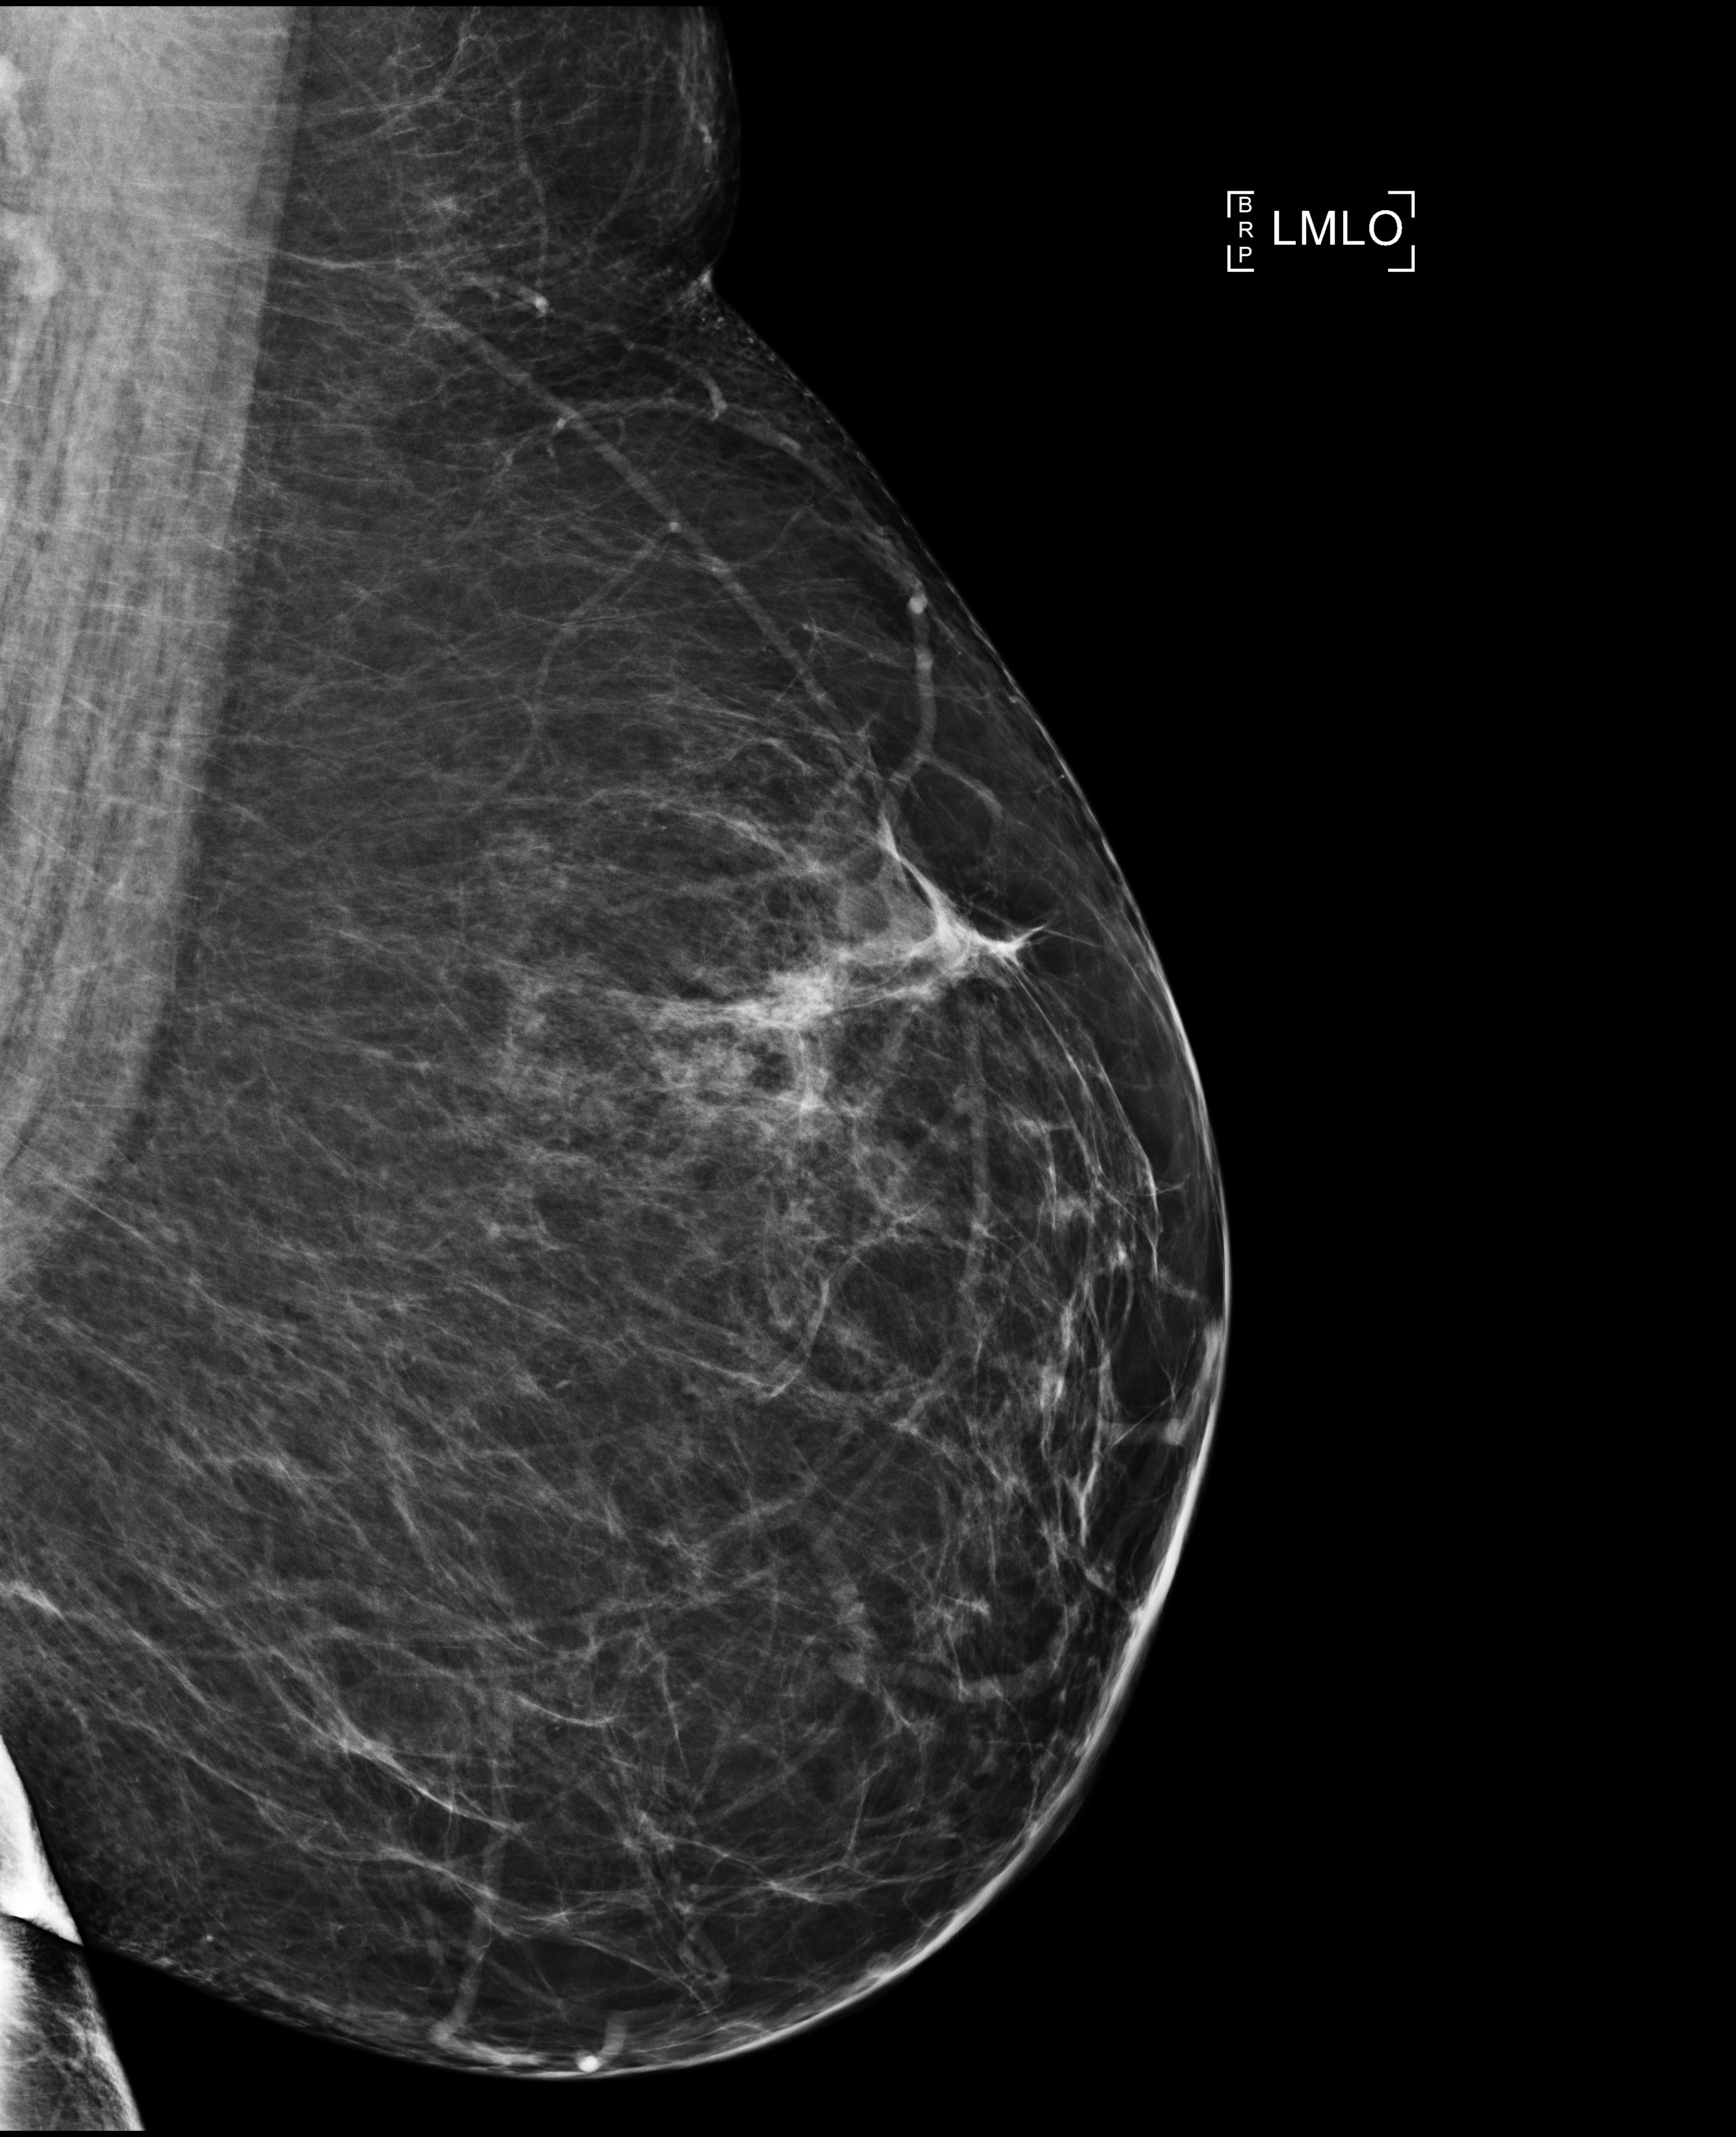
Annual screening mammography examination. Patient: female, 51 years.
Image type: full-field digital mammogram. Breast: left. Projection: medio-lateral oblique projection.